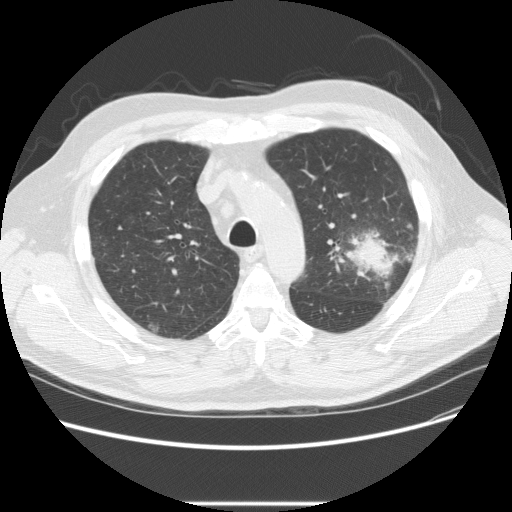
Low-dose screening chest CT, one axial slice; 120 kVp; lung window (W 1500 / L -600 HU); 512 × 512 image matrix.
Annotated regions visible in this slice (expert manual segmentation):
- lesion 1 (tumor, upper lobe of left lung): bounding box [x1, y1, x2, y2] px = [343, 235, 395, 280]